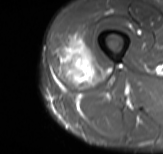
MRI of an extremity soft-tissue mass, one axial slice; STIR; MR volume resampled by the dataset authors to the PET/CT grid (not the native acquisition matrix); 163 × 154 image matrix. Male patient. From the clinical record (not read from this slice): histological type: poorly differentiated synovial sarcoma; grade: high; site of the primary tumour: right buttock.
Structures marked on this image (expert contour drawn on MRI and transferred to this co-registered scan by the dataset authors):
- gross tumour volume including surrounding oedema: bounding box (x1, y1, x2, y2) in pixels: (59, 34, 106, 90)
- gross tumour volume (mass): (62, 39, 85, 83)